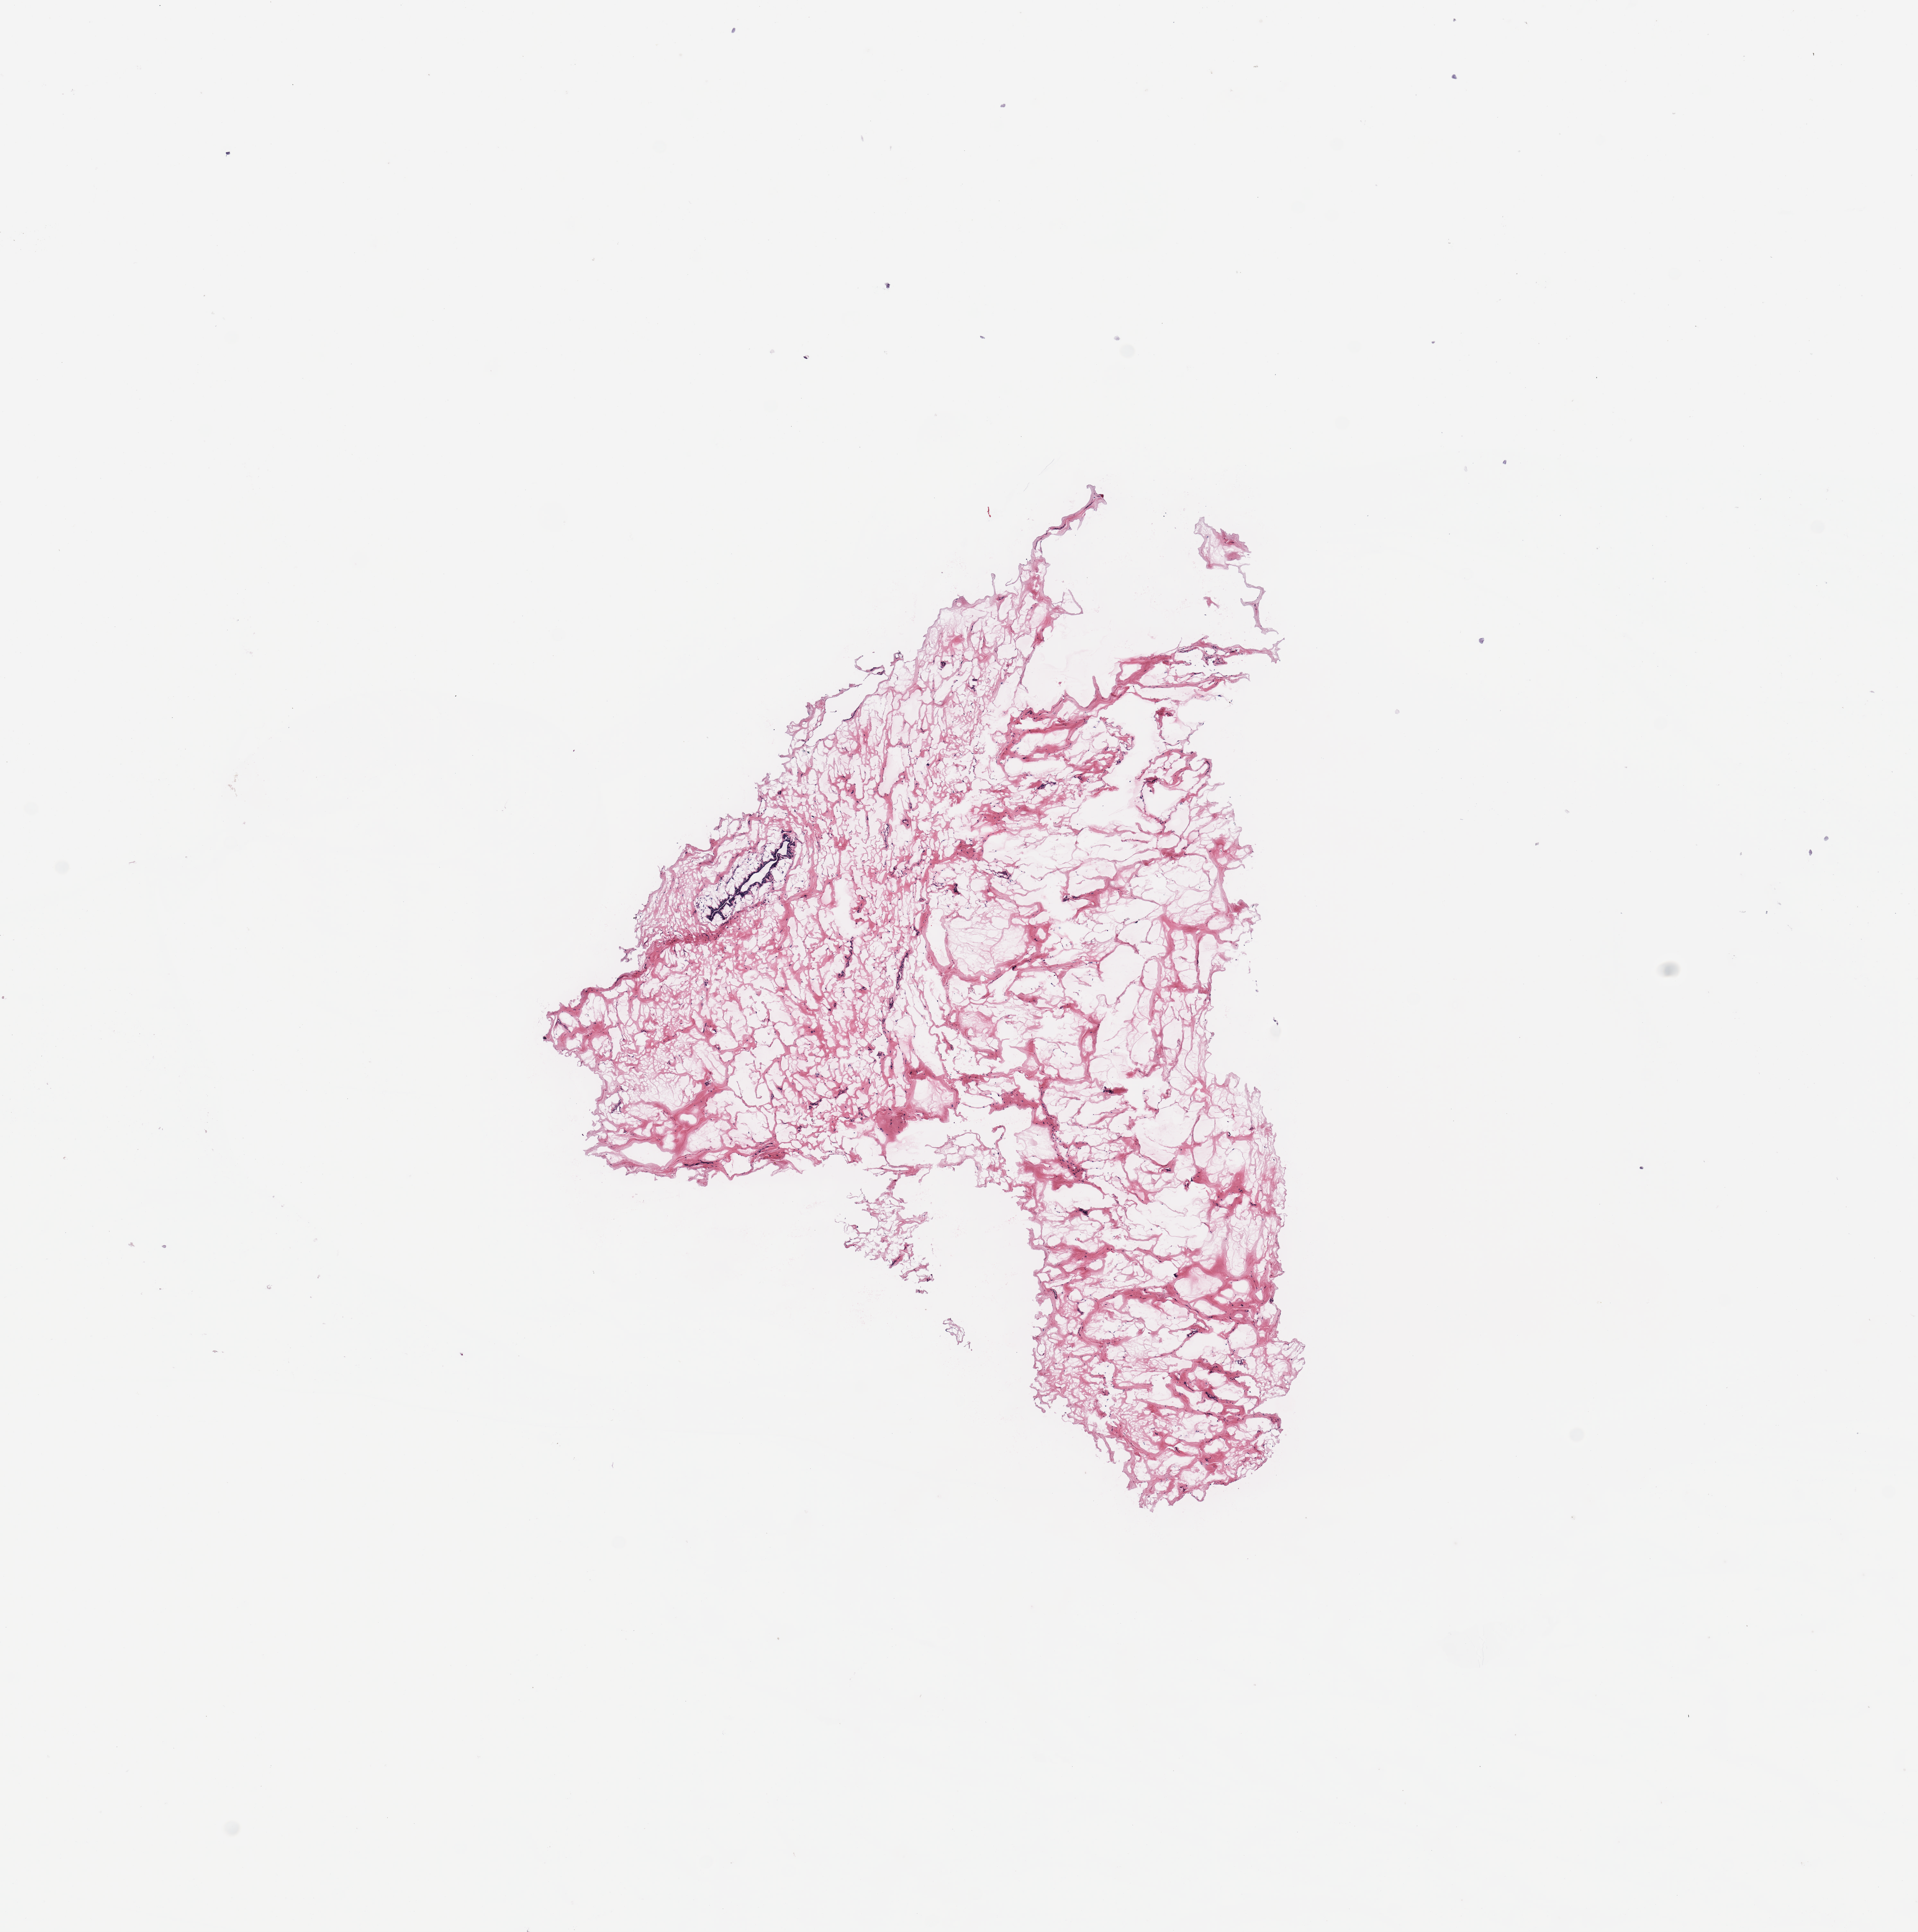
Digitized H&E-stained tissue section (whole slide), a low-resolution overview of the entire scanned area, about 11.8 x 11.9 mm (from a 20x scan); breast, tissue type not recorded.
Patient diagnosis (cohort enrolment): breast cancer (breast).